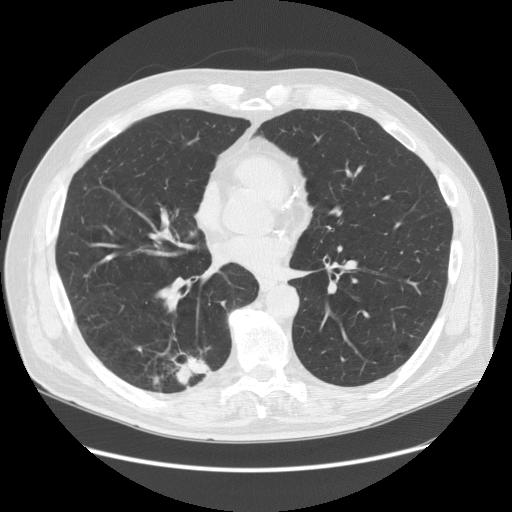
Low-dose screening chest CT, one axial slice; position 68 of 149 along the scan axis; reconstruction kernel STANDARD; 120 kVp; lung window (W 1500 / L -600 HU); 2.5 mm slice thickness; 512 × 512 image matrix, field of view 400 × 400 mm.
Outlined on this slice (expert manual segmentation):
- lesion 1 (tumor, lower lobe of right lung): bounding box (x1, y1, x2, y2) in pixels: (174, 354, 211, 385)